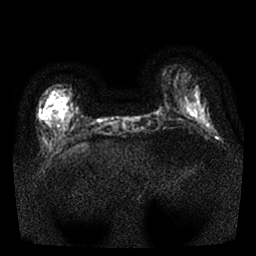
Breast MRI, one axial slice. Diffusion-weighted series; image 2 of 4 stored at this slice position (different b-values; order by instance number). 1.5 T. 4 mm slice thickness. 256 × 256 image matrix, field of view 310 × 310 mm. Female patient.
Annotated regions visible in this slice (expert manual segmentation):
- tumour on diffusion-weighted imaging: bounding box (x1, y1, x2, y2) in pixels: (39, 109, 44, 119)